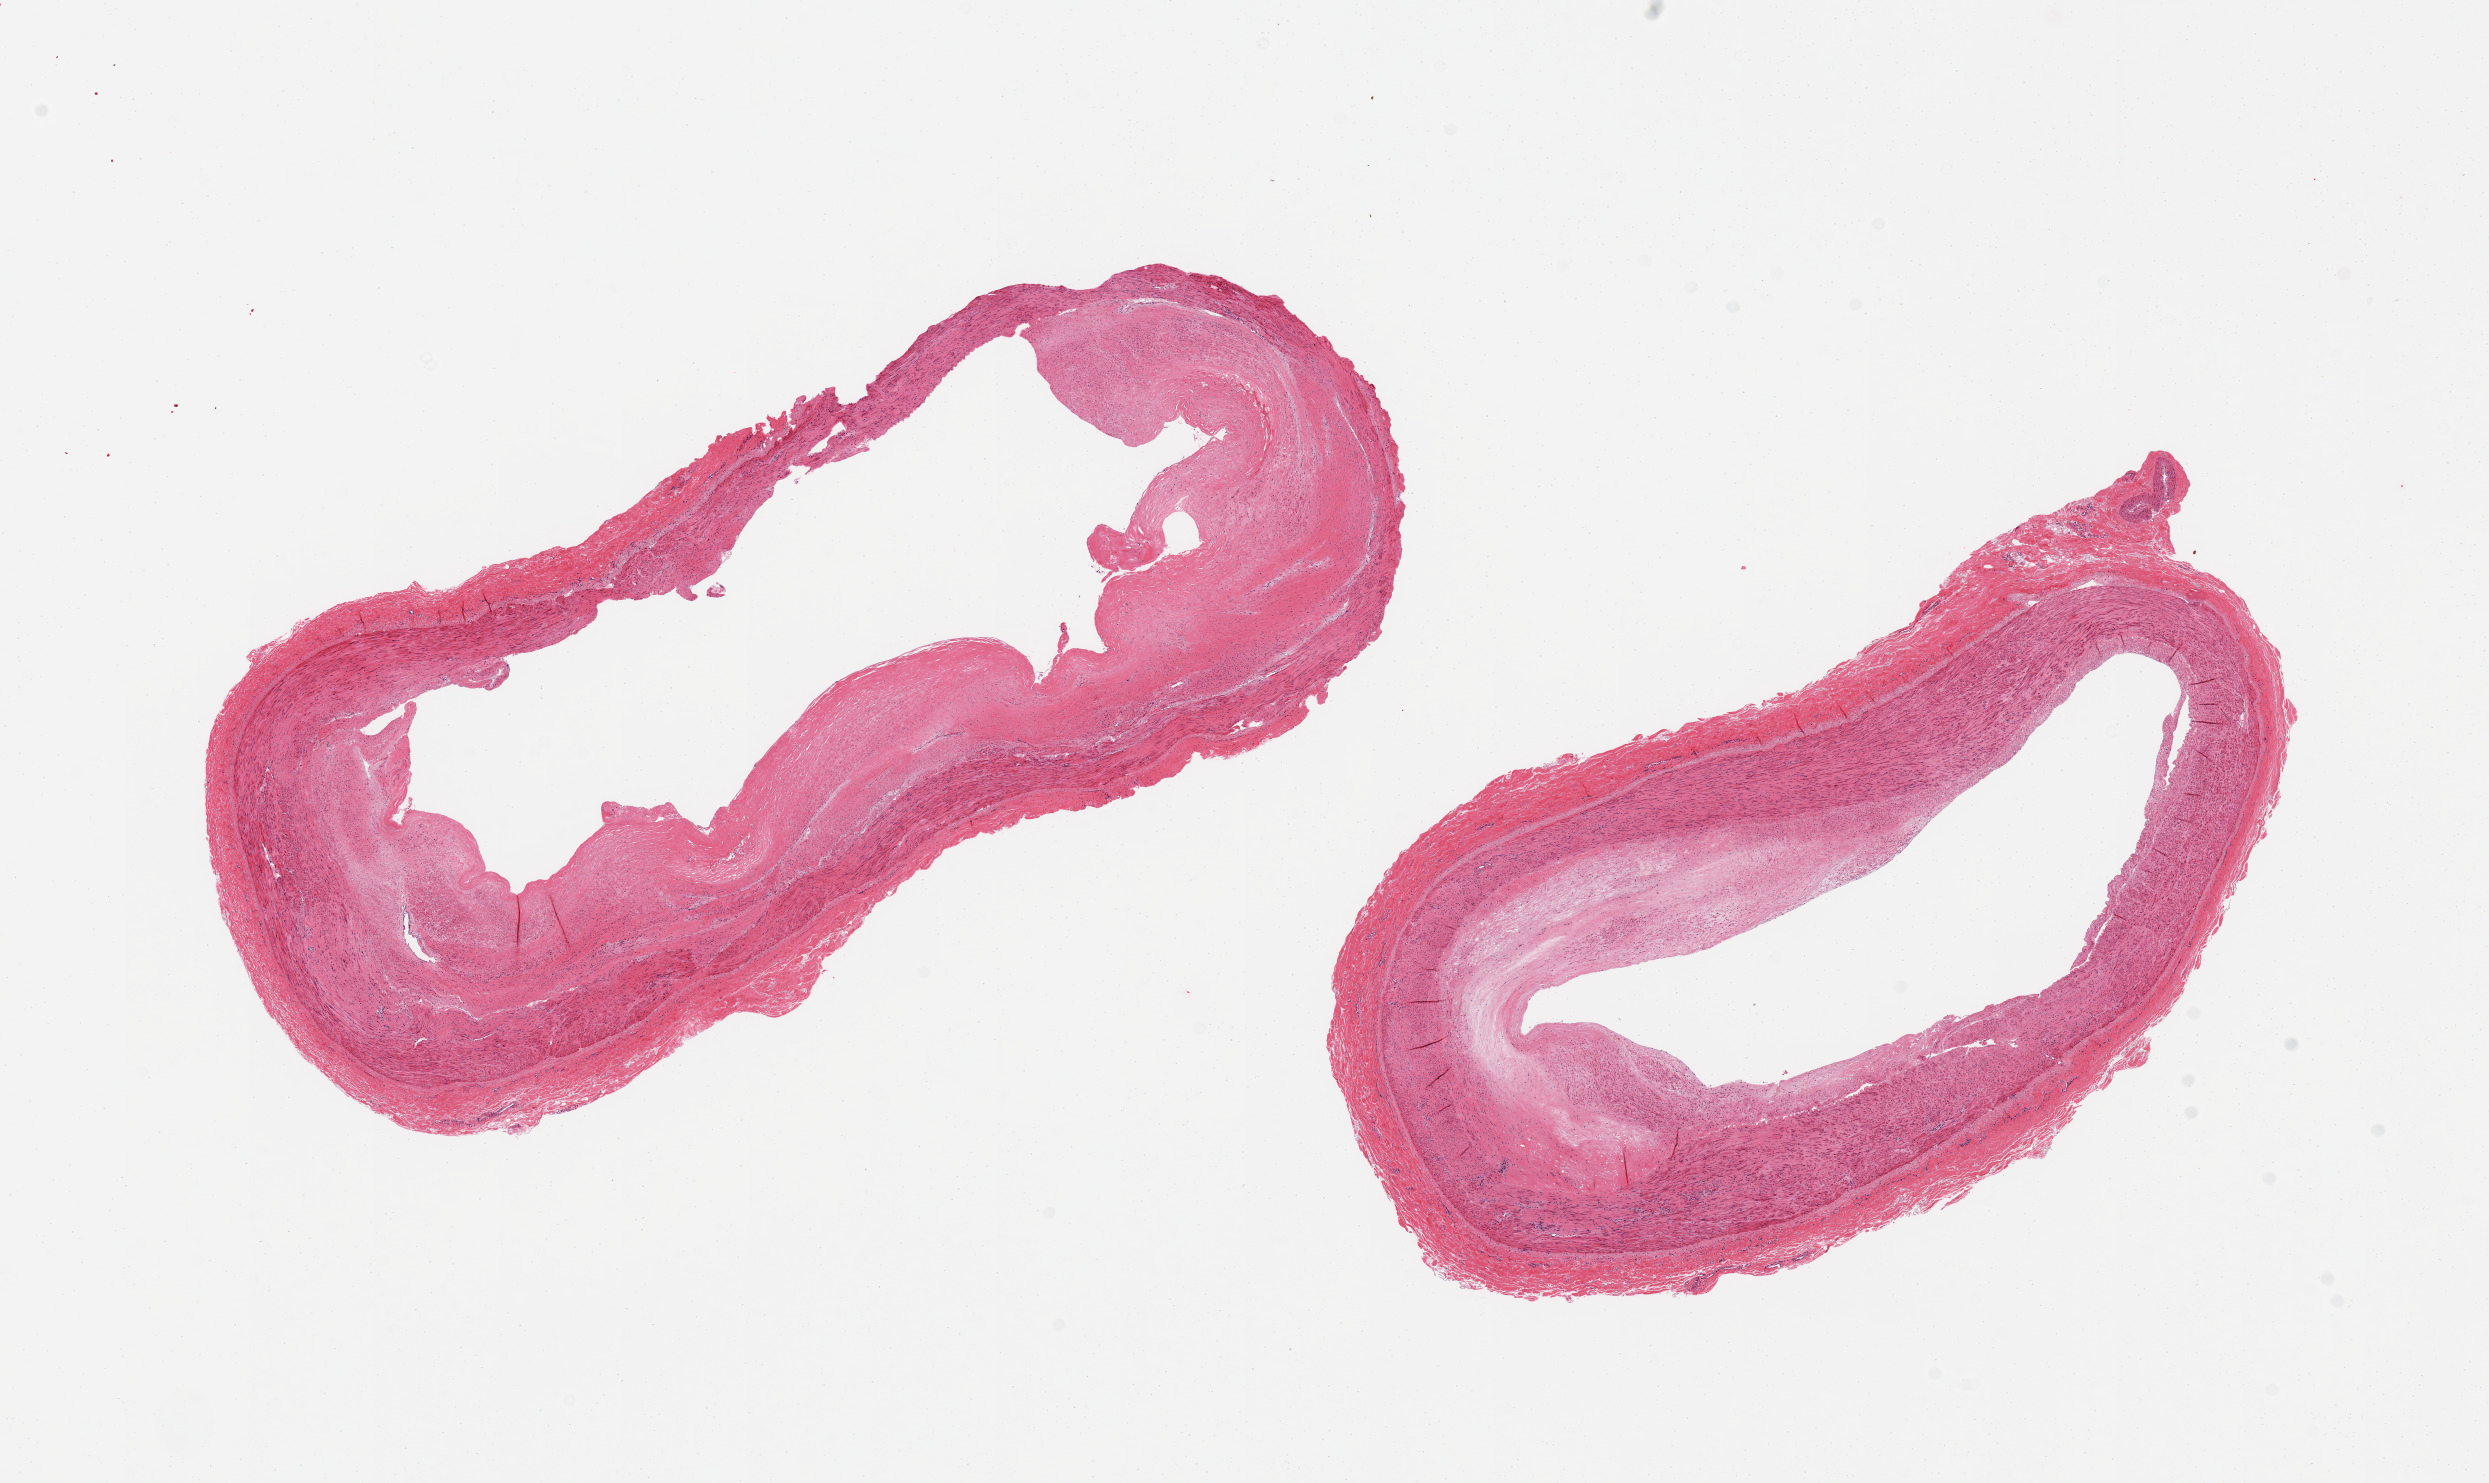
Hematoxylin and eosin (H&E) whole-slide image — whole scanned area (about 19.7 x 11.7 mm, from a 20x scan) shown as a low-resolution overview; PAXgene-fixed paraffin-embedded (PFPE) section; sampled site (target tissue): tibial artery; tissue donor sample. Donor: male.
* pathologist's review note for this sample: 2 pieces; eccentric fibrofatty plaques; well trimmed